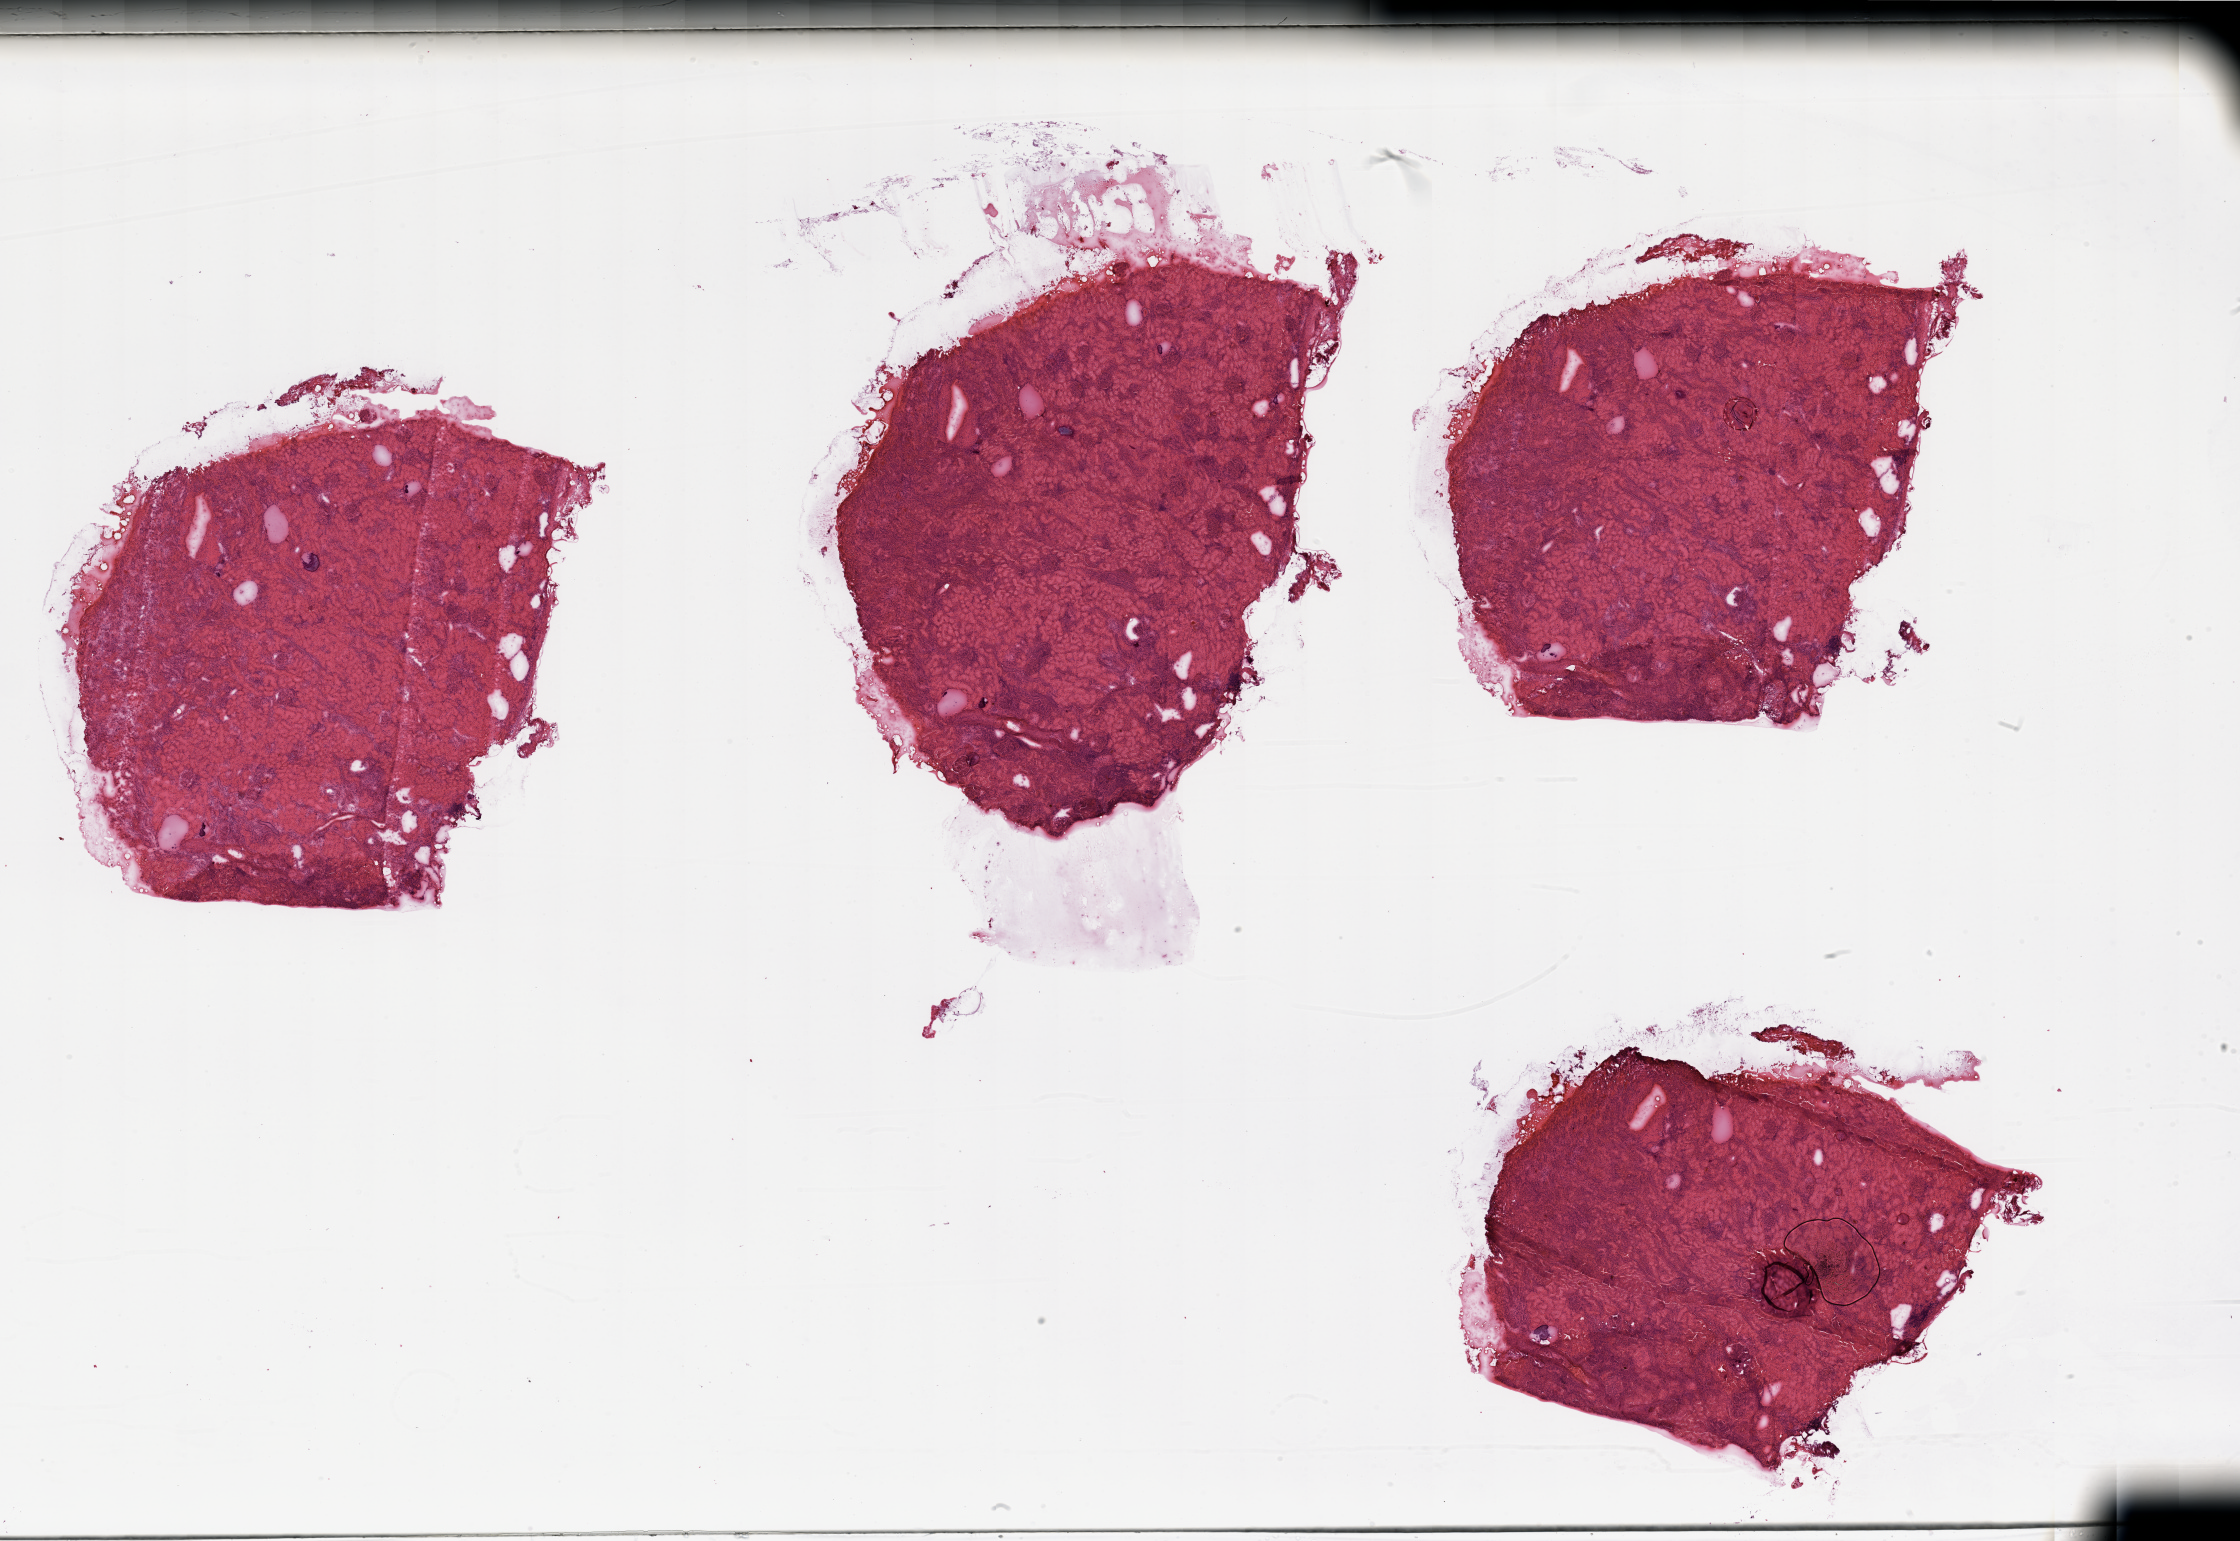
Whole-slide histology image, Hematoxylin and eosin (H&E) stained — whole scanned area (about 35.4 x 24.4 mm, from a 20x scan) shown as a low-resolution overview. Normal (non-tumour) tissue sample, sampled site: kidney. Patient: male, age 67 years.
This section: normal (non-tumour) tissue from the same patient. Patient diagnosis: Renal cell carcinoma, NOS.